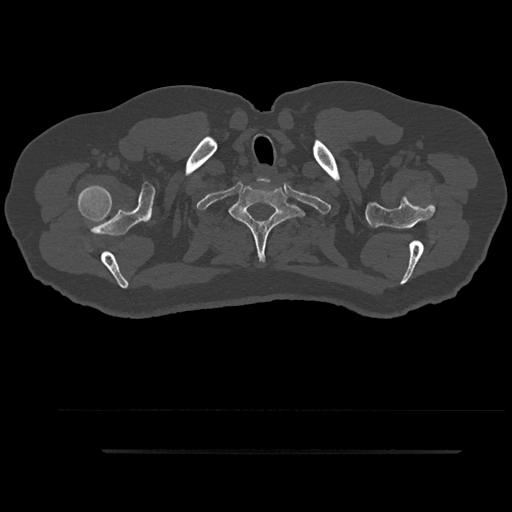
CT including the spine, one axial slice. Position 797 of 797 along the scan axis. 120 kVp. Bone window (W 1800 / L 400 HU). 0.5 mm slice thickness. 512 × 512 image matrix, field of view 432 × 432 mm. Male patient, age 63 years. Case-level facts recorded for this patient, not image findings: primary cancer: renal; vertebrae with lytic lesions (as recorded): T8.
Outlined on this slice (semi-automatically segmented with operator editing):
- T1 vertebra: bounding box <230,185,304,260> (left, top, right, bottom; pixels)
- T2 vertebra: <215,224,301,232>